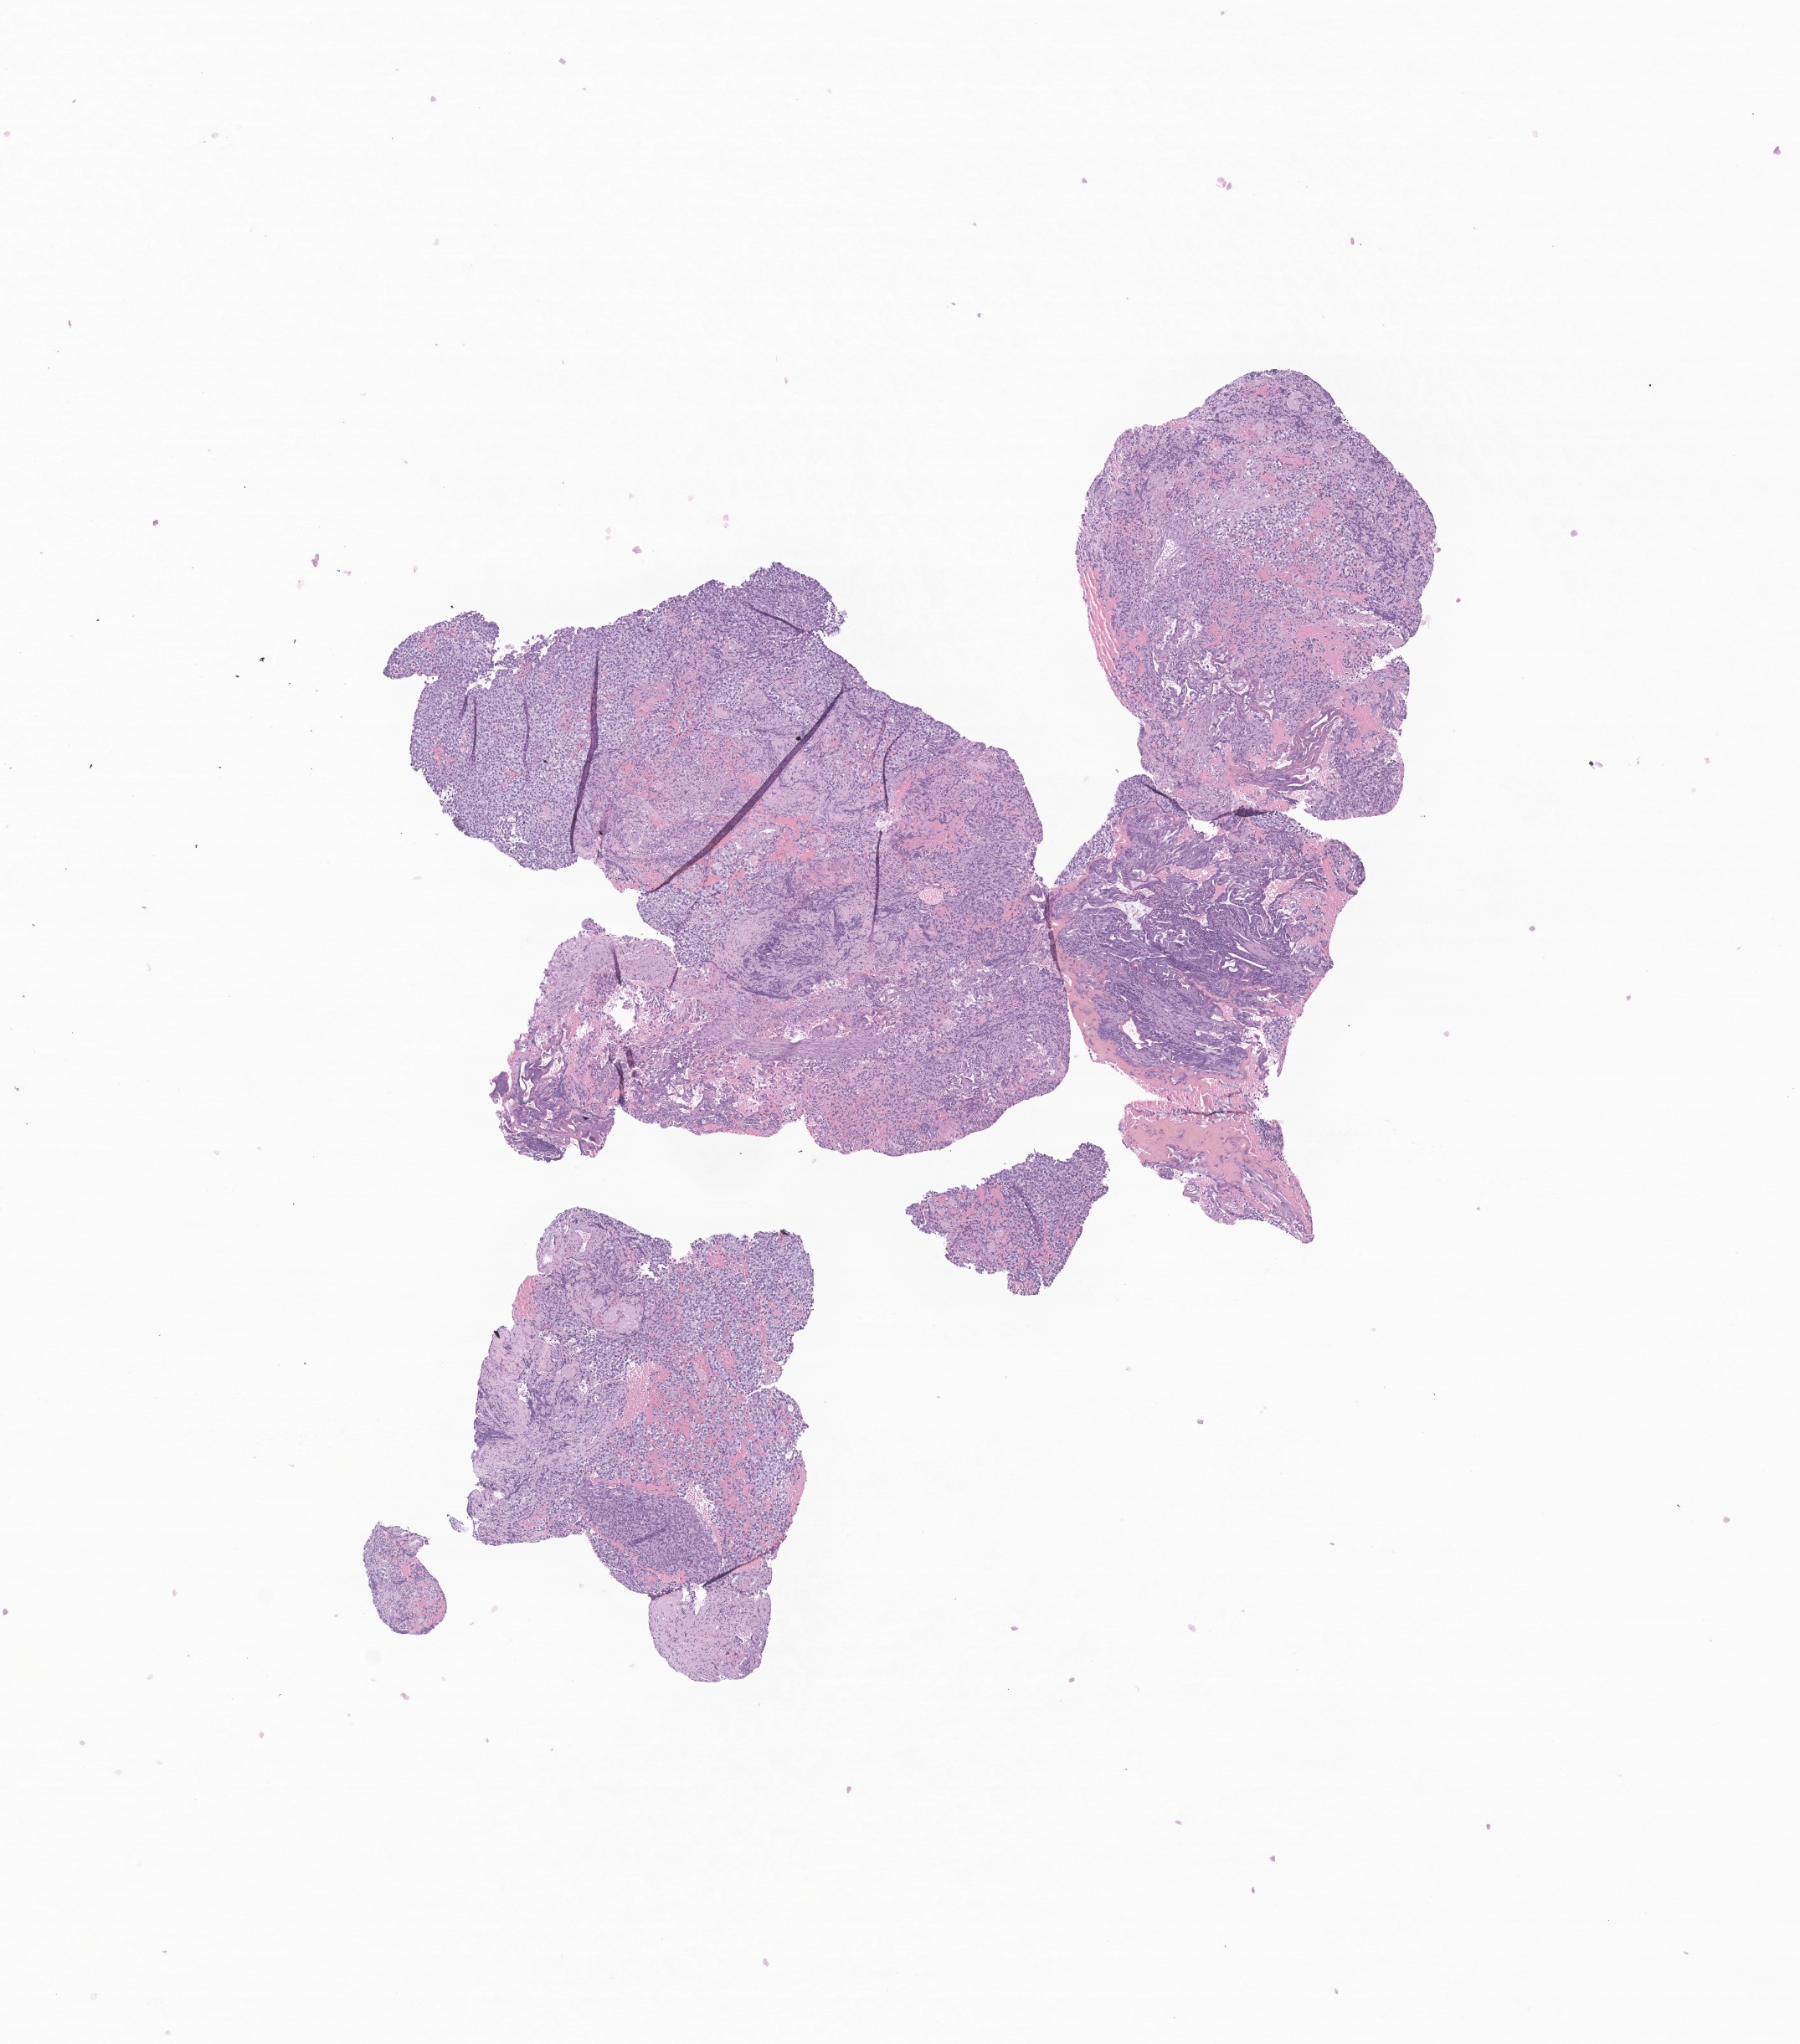
Digitized hematoxylin and eosin (H&E)-stained section of tumor tissue from the brain, a low-resolution overview of the entire scanned area, about 9.1 x 10.3 mm; FFPE section. Patient male; age 207 months (17 years 3 months).
Recorded diagnosis: Germinoma.